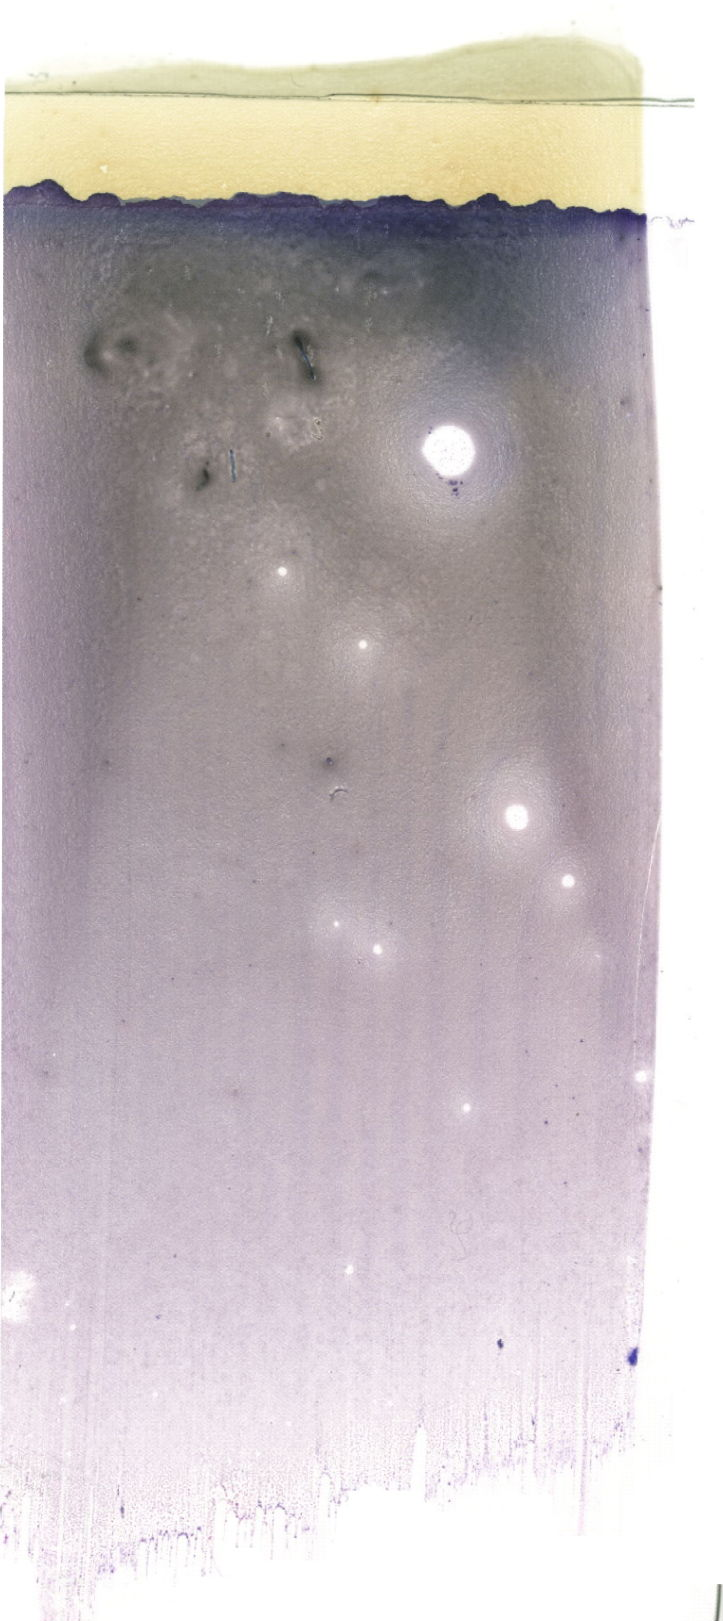
Whole-slide image of a May-Grünwald-Giemsa (MGG)-stained bone marrow aspirate smear, a low-resolution overview of the entire scanned area, about 20.5 x 45.9 mm. Patient sex: female.
Diagnosis: Acute Megakaryoblastic Leukemia.